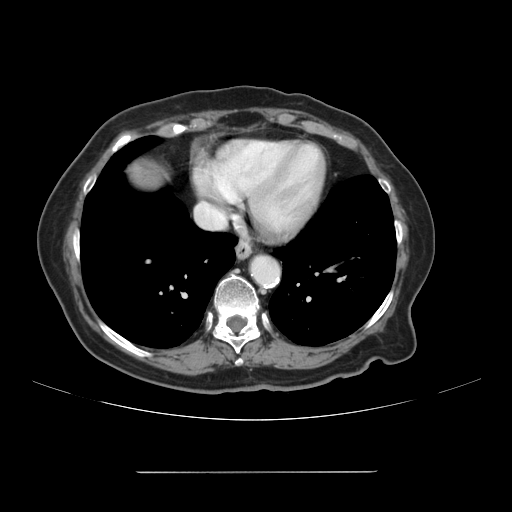
Contrast-enhanced abdominal CT, one axial slice; position 110 of 111 along the scan axis; intravenous contrast given; soft-tissue window (W 400 / L 40 HU); 2.5 mm slice thickness; 512 × 512 image matrix, field of view 400 × 400 mm. Female patient, age 74 years. Case-level facts recorded for this patient, not image findings: diagnosis: colorectal cancer liver metastases, imaged before liver resection; multiple liver metastases: yes; largest metastasis: 1.1 cm; disease in both lobes: yes.
Structures marked on this image (outlined manually by an expert reader):
- liver: bounding box <124,159,168,194> (left, top, right, bottom; pixels)